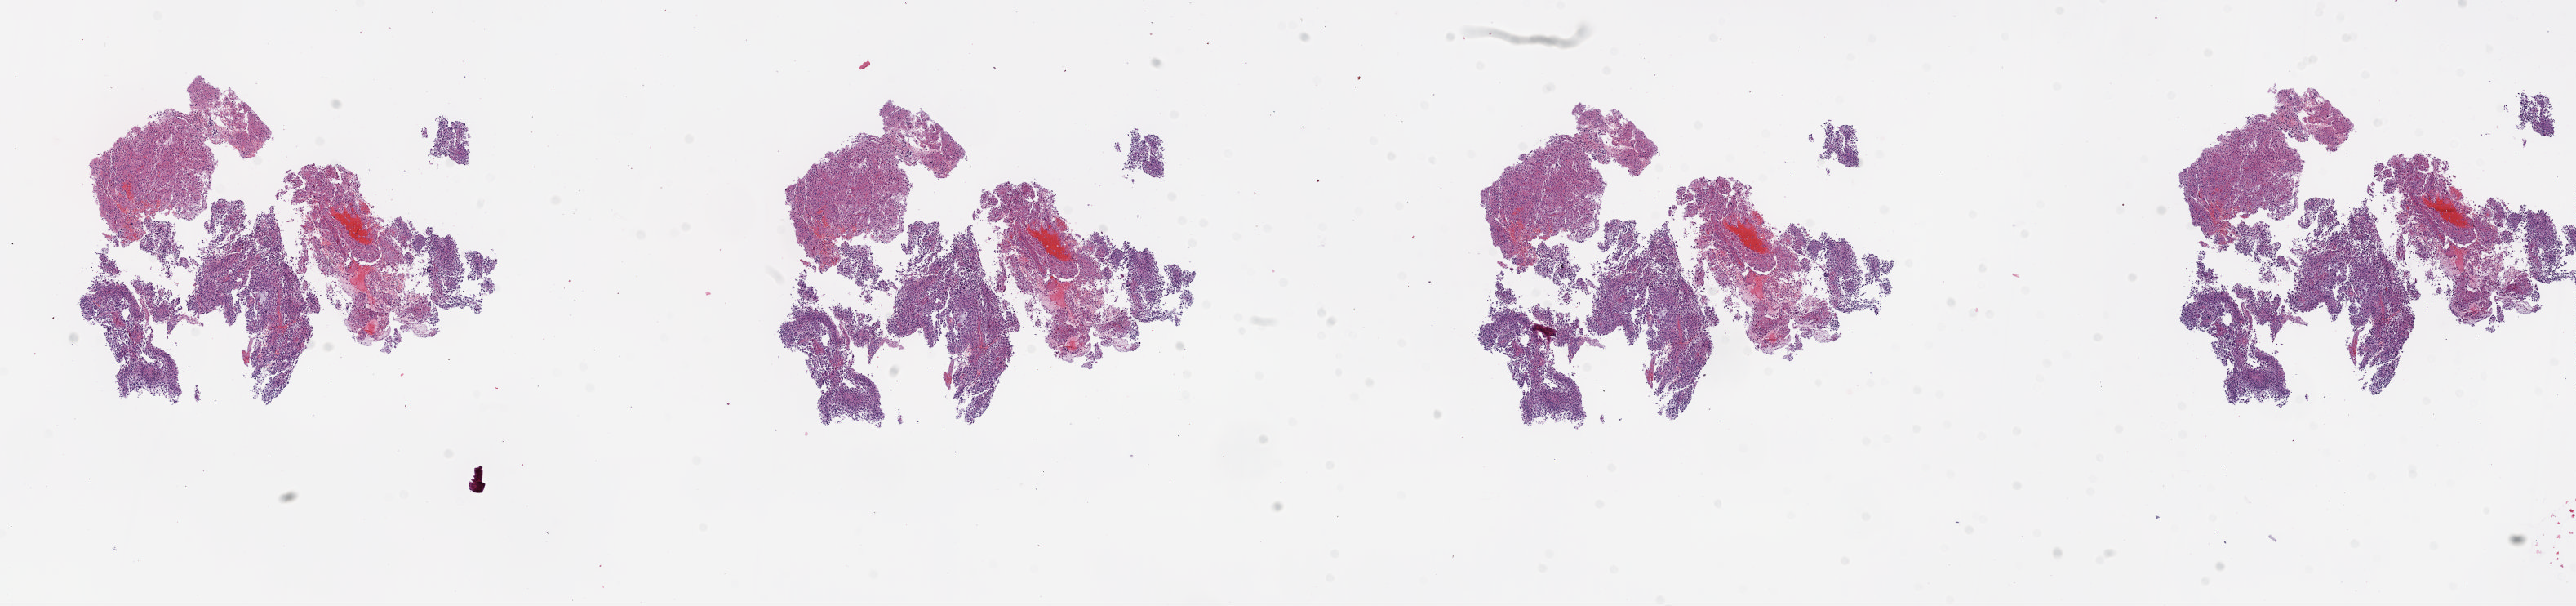
Digitized Hematoxylin and eosin (H&E) stained tissue section (whole slide) — a low-resolution overview of the entire scanned area, about 25.3 x 5.9 mm (from a 5x scan). Frozen section from the top of the tissue portion. Brain, primary tumour sample. Patient: female, age at initial diagnosis 23 years. Slide review estimates, as recorded: tumour cells 100%, tumour nuclei 85%, normal cells 0%, stromal cells 0%, necrosis 0%.
Histologic diagnosis: Glioblastoma.